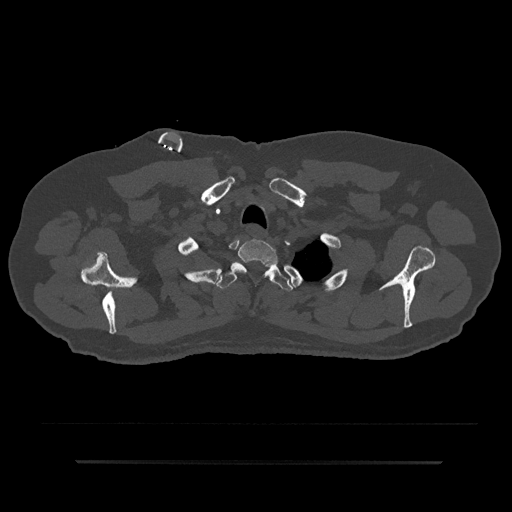
CT including the spine, one axial slice. Position 716 of 797 along the scan axis. Reconstruction kernel Br40s/3. Bone window (W 1800 / L 400 HU). 0.5 mm slice thickness. 512 × 512 image matrix. Patient: male, 59 years. From the clinical record (not read from this slice): primary cancer: bile ducts; vertebrae with lytic lesions (as recorded): T10.
Outlined on this slice (semi-automatic segmentation, software-assisted and operator-edited):
- T1 vertebra: box from (x=231, y=239) to (x=278, y=276) px
- T2 vertebra: (x=215, y=263)–(x=293, y=291)